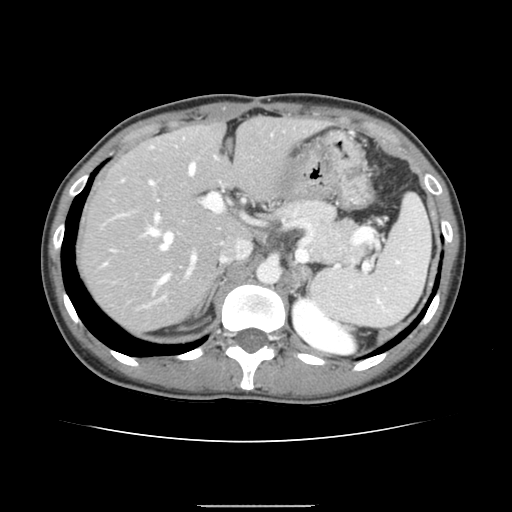
Contrast-enhanced abdominal CT, one axial slice; slice 100 of 150 in the series (ordered by position); 120 kVp; intravenous contrast given; soft-tissue window (W 400 / L 40 HU); 512 × 512 image matrix, field of view 324 × 324 mm. Female patient, age 32 years. From the clinical record (not read from this slice): diagnosis: colorectal cancer liver metastases, imaged before liver resection; multiple liver metastases: yes; largest metastasis: 0.7 cm; chemotherapy before resection: yes.
Annotated regions visible in this slice (expert manual segmentation):
- hepatic veins: box from (x=148, y=163) to (x=195, y=283) px
- liver: (x=81, y=118)–(x=315, y=331)
- planned liver remnant (the part of the liver to remain after resection): (x=81, y=118)–(x=319, y=281)
- portal vein (with intrahepatic branches): (x=104, y=181)–(x=222, y=274)